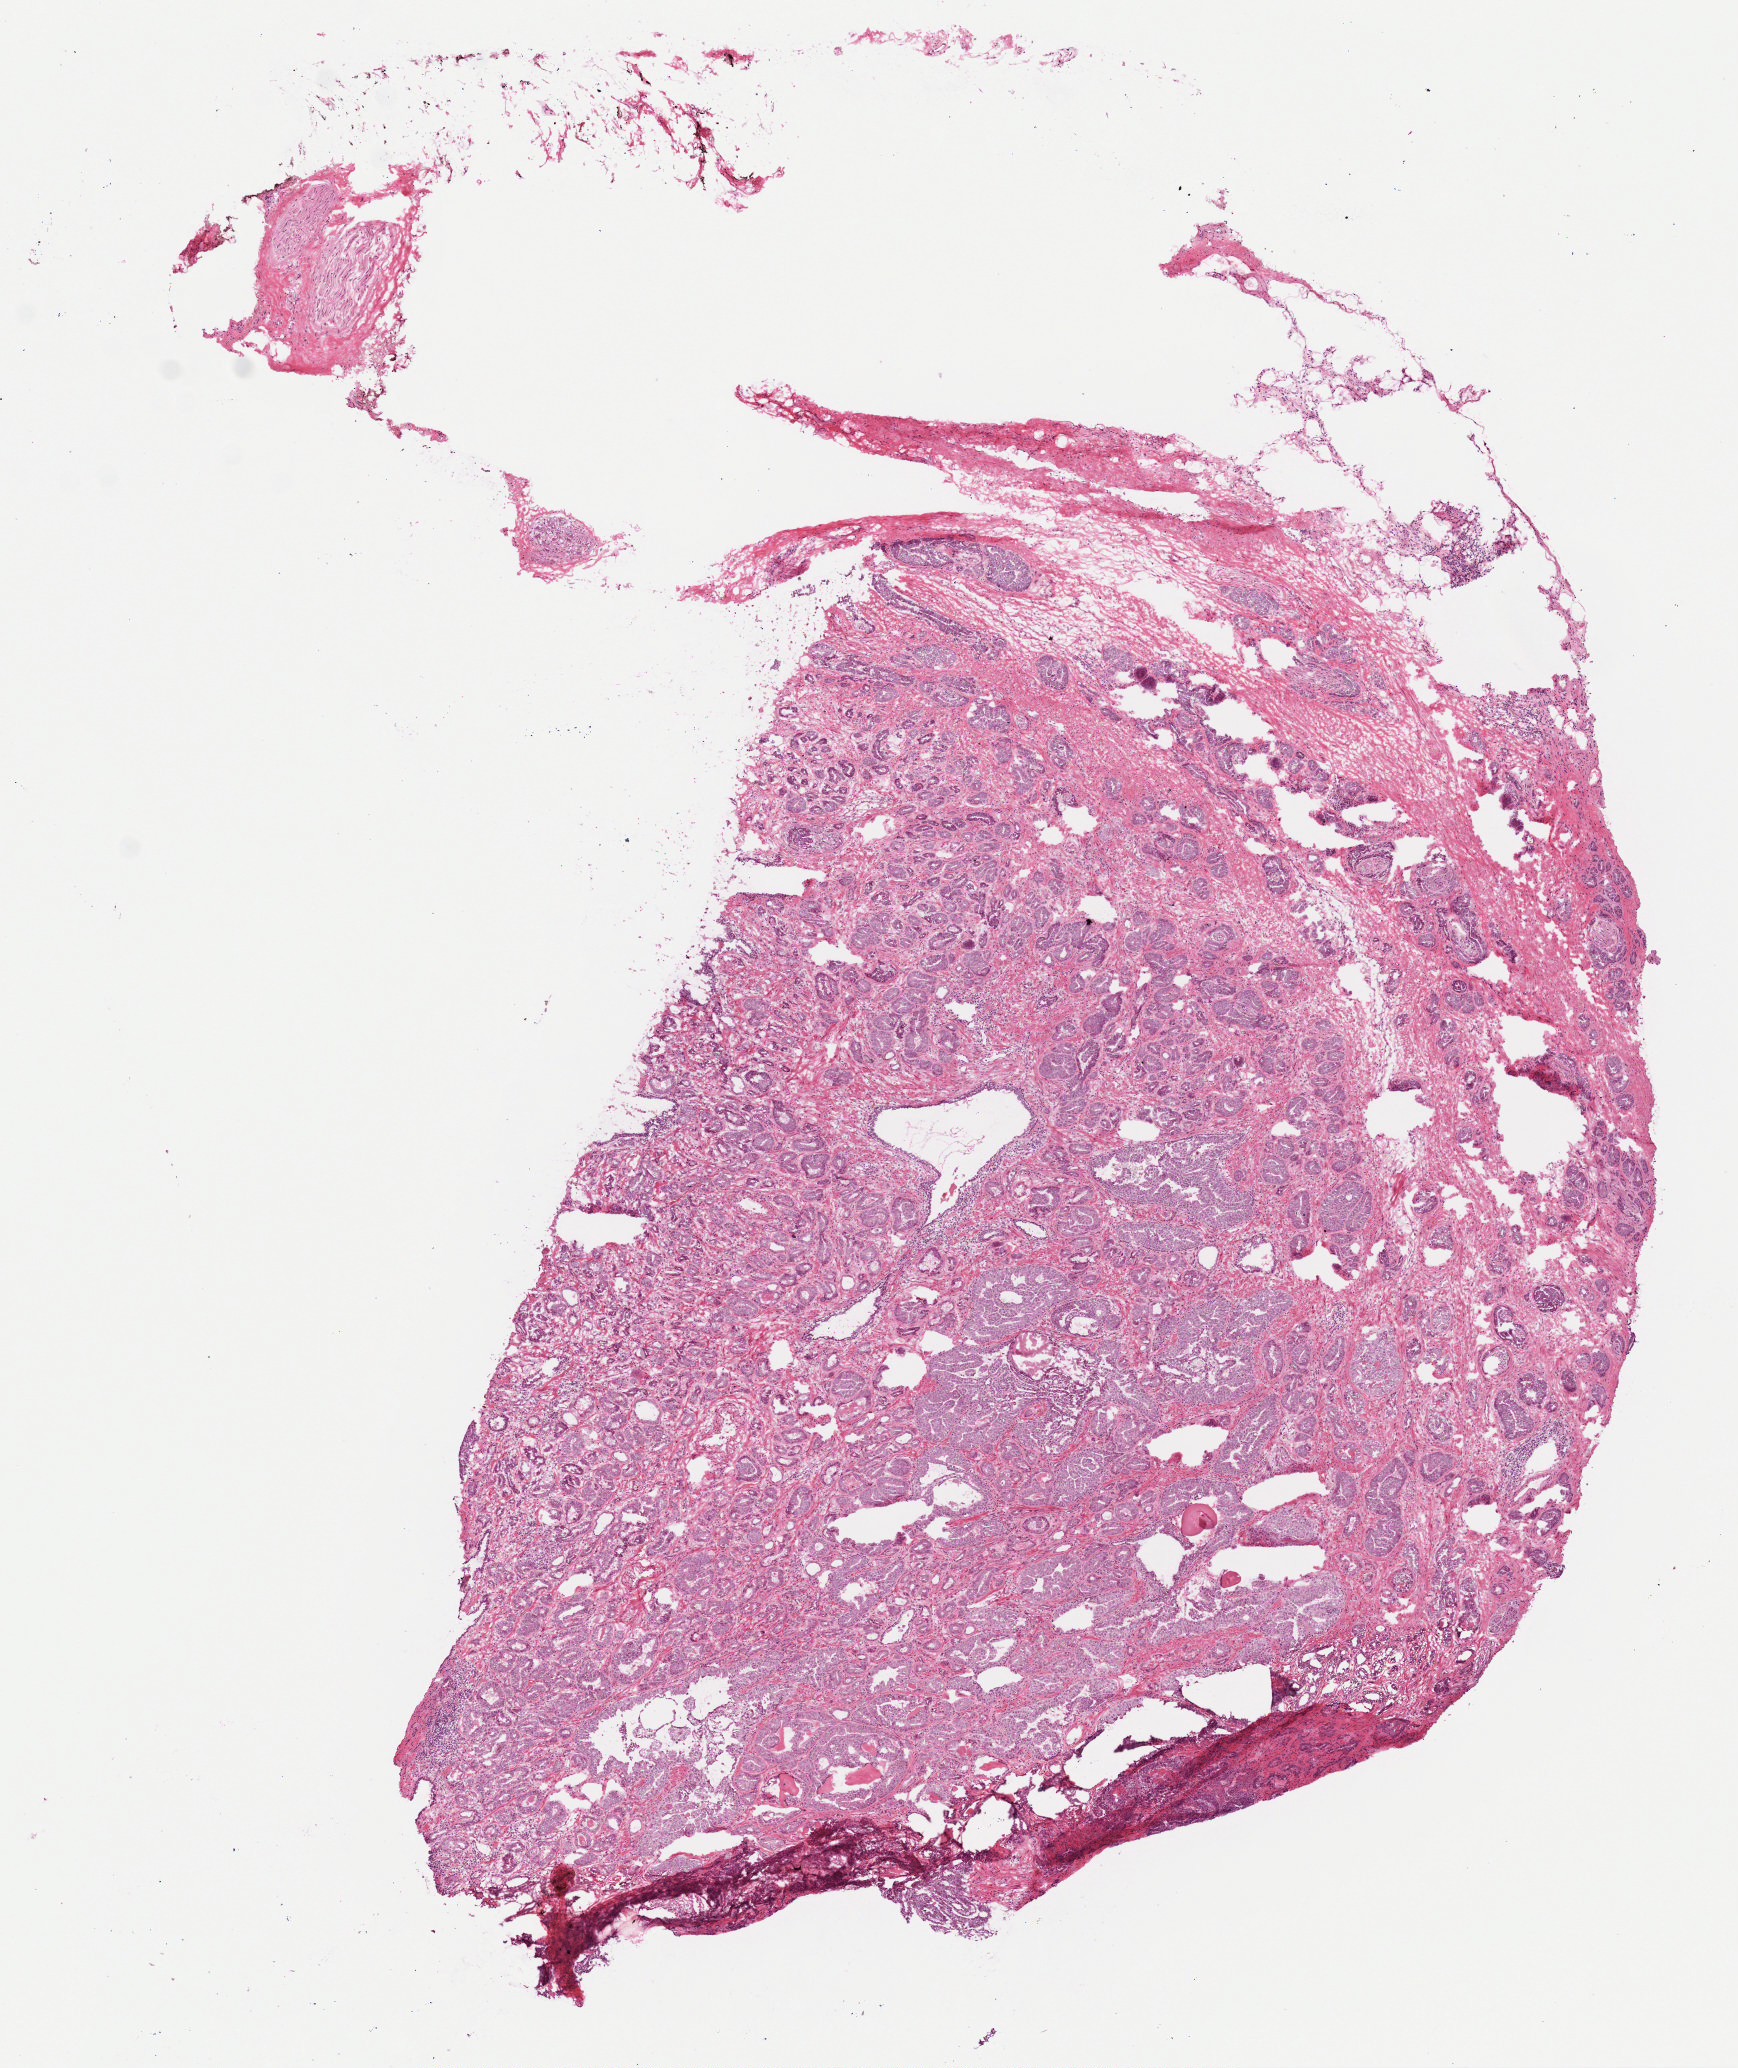
Whole-slide histology image, Hematoxylin and eosin (H&E) stained, a low-resolution overview of the entire scanned area, about 7.0 x 8.3 mm; frozen section; sample: primary tumour, prostate. Male patient; age at initial diagnosis 64 years. Gleason score: 7 (3+4). Composition of this section per pathologist review: tumour cells 80%, tumour nuclei 85%, normal cells 5%, stromal cells 15%, necrosis 0%. Infiltration values recorded for this section: lymphocyte infiltration 0%, monocyte infiltration 0%, neutrophil infiltration 0%.
* lymph nodes positive (case pathology): 0 of 3 examined
* diagnosis: Adenocarcinoma, NOS (prostate gland)
* laterality: bilateral